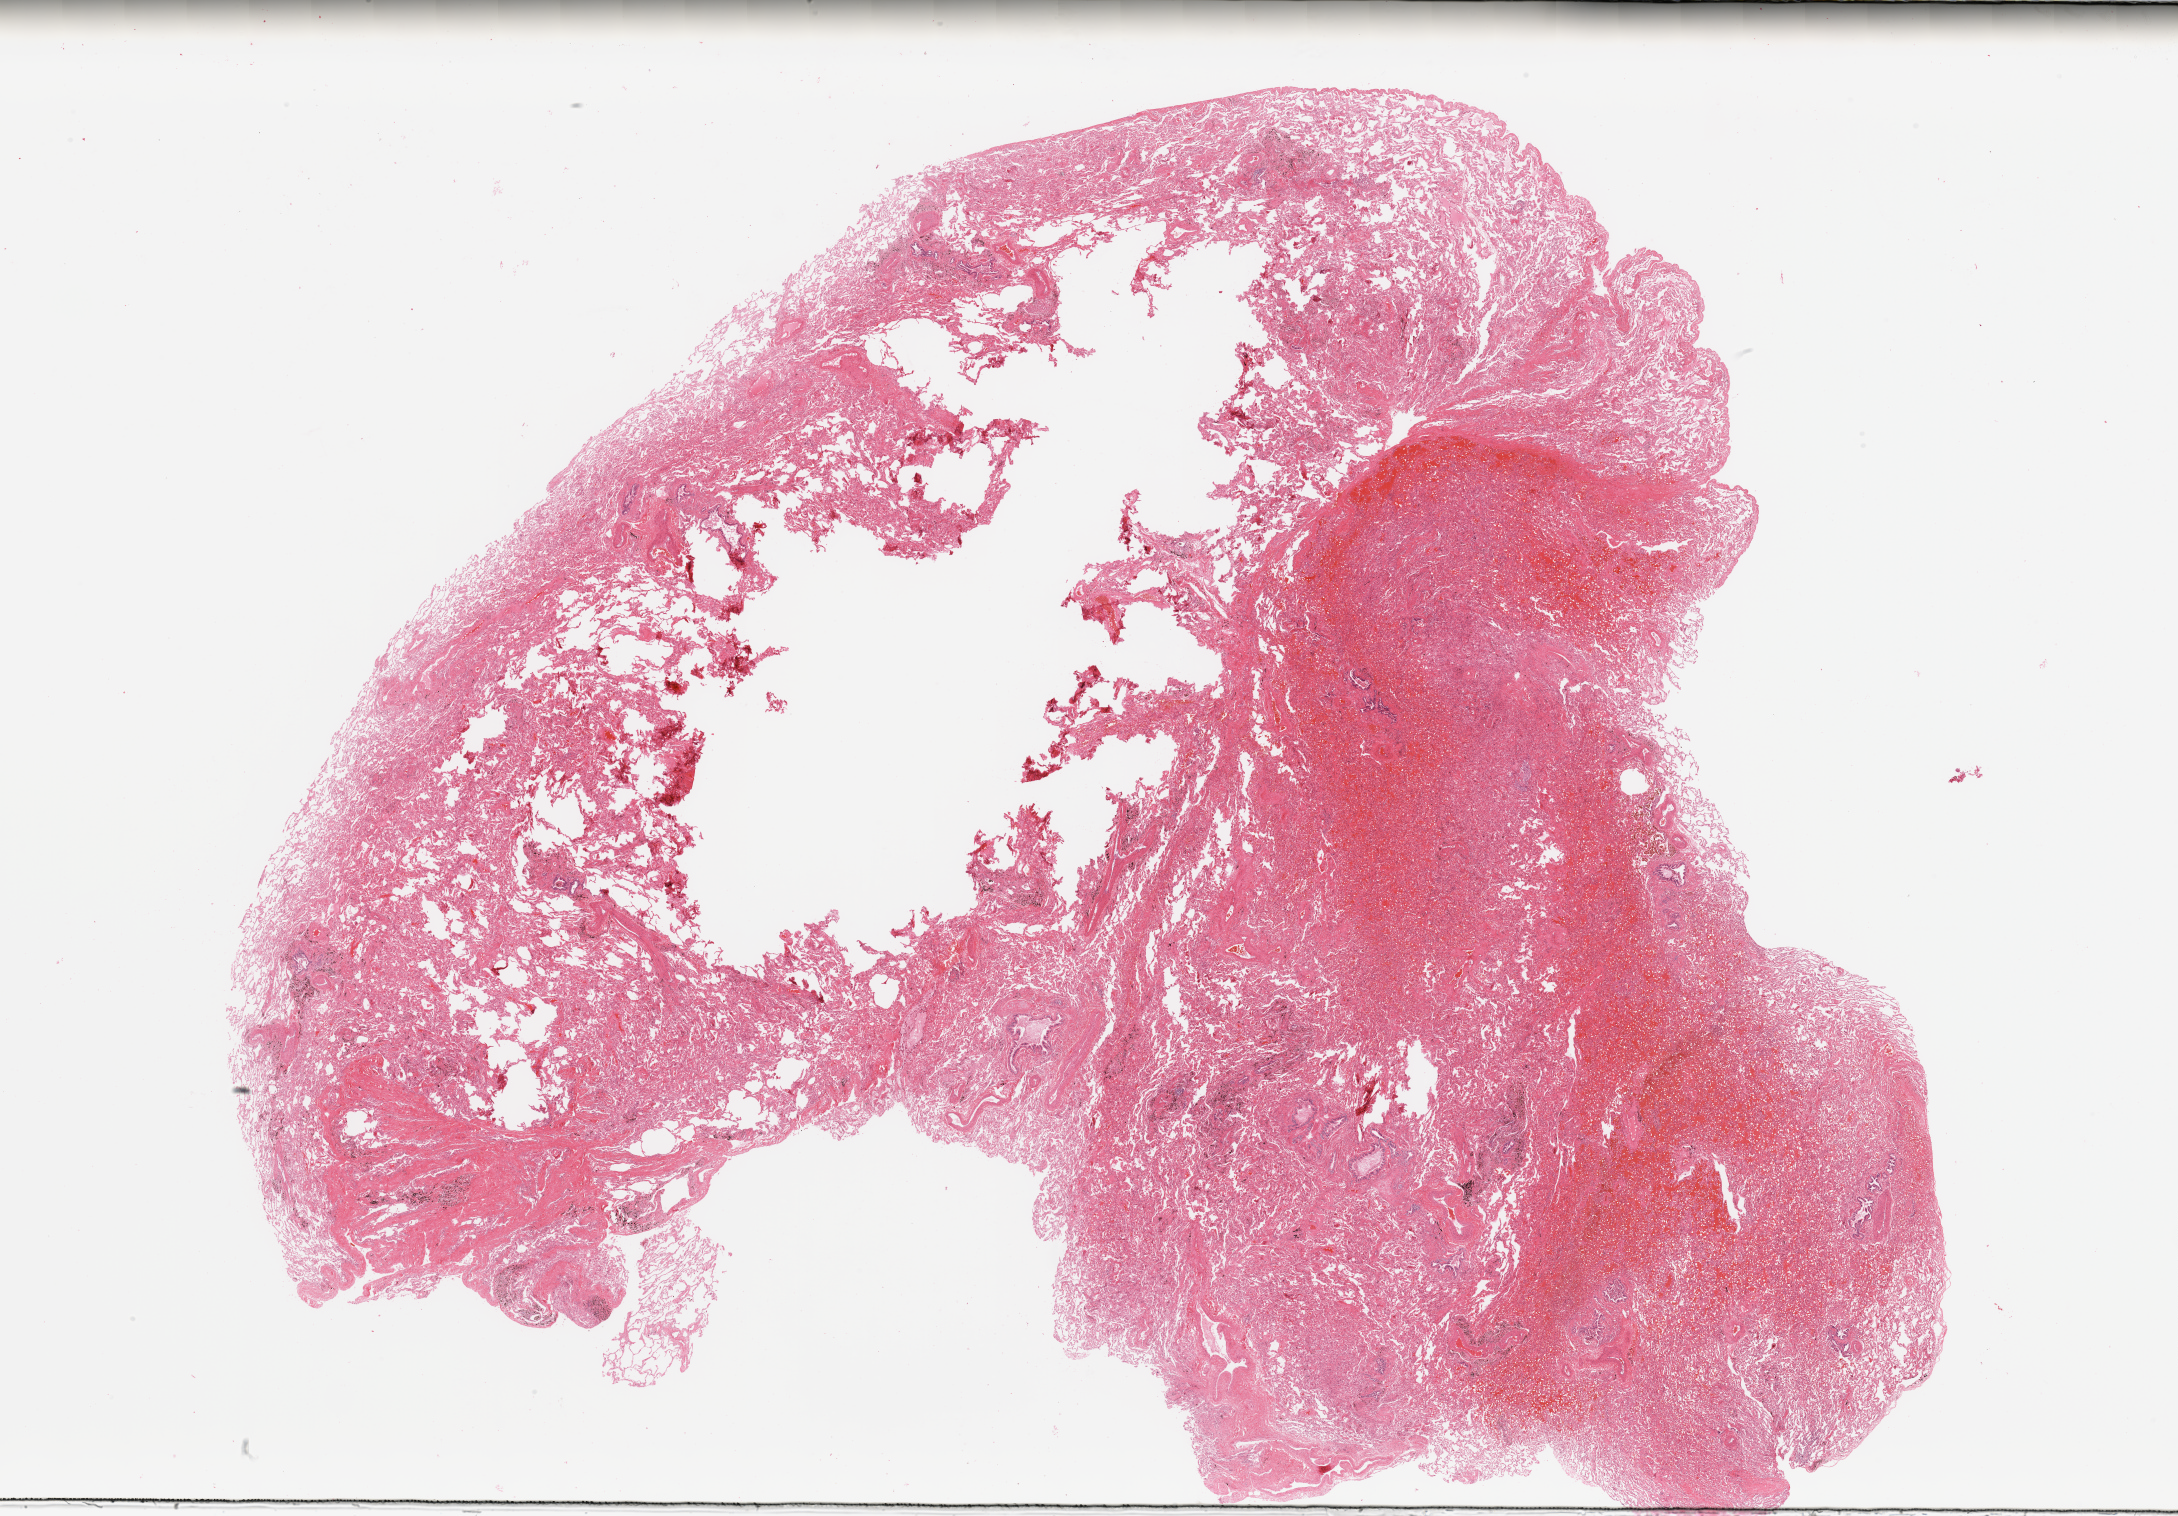
Digitized Hematoxylin and eosin (H&E) stained tissue section (whole slide), whole scanned area (about 34.5 x 24.0 mm) shown as a low-resolution overview, normal (non-tumour) tissue sample, sampled site: lung. Patient: female, age 65 years.
• this section: normal (non-tumour) tissue from the same patient
• patient diagnosis: Adenocarcinoma, NOS